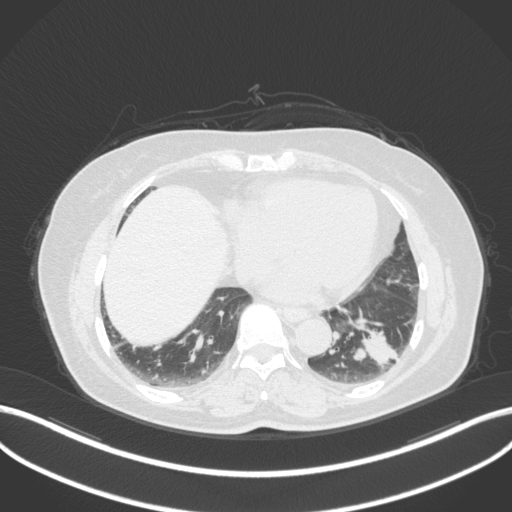
Chest CT, one axial slice. Slice 126 of 307 in the series (ordered by position). Reconstruction kernel B31f. 120 kVp. Lung window (W 1500 / L -600 HU). 1 mm slice thickness. 512 × 512 image matrix. Female patient, age 59 years. Case-level facts recorded for this patient, not image findings: clinical TNM (as recorded): T2a N0 M0; histopathological grade: G2-3.
Outlined on this slice (rectangle marked by the reading radiologist):
- lung tumour (recorded histology: adenocarcinoma): bounding box [x1, y1, x2, y2] px = [349, 324, 401, 374]